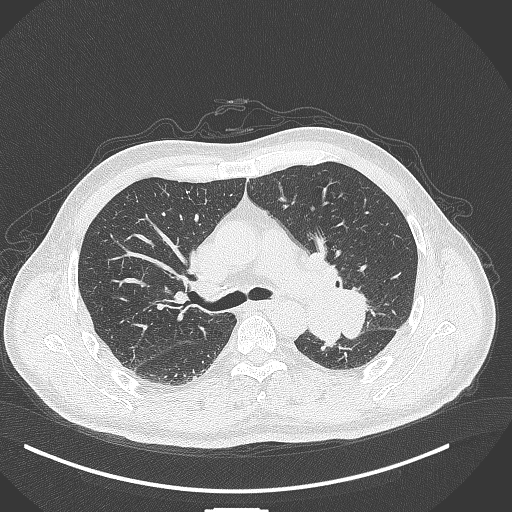
Chest CT, one axial slice; position 269 of 429 along the scan axis; reconstruction kernel B70f; 120 kVp; lung window (W 1500 / L -600 HU); 1 mm slice thickness; 512 × 512 image matrix. Male patient, age 55 years. Case-level facts recorded for this patient, not image findings: clinical TNM (as recorded): T3 N0 M1c; histopathological grade: G3.
Annotated regions visible in this slice (bounding box drawn by a radiologist):
- lung tumour (recorded histology: adenocarcinoma): bounding box (x1, y1, x2, y2) in pixels: (306, 273, 369, 348)